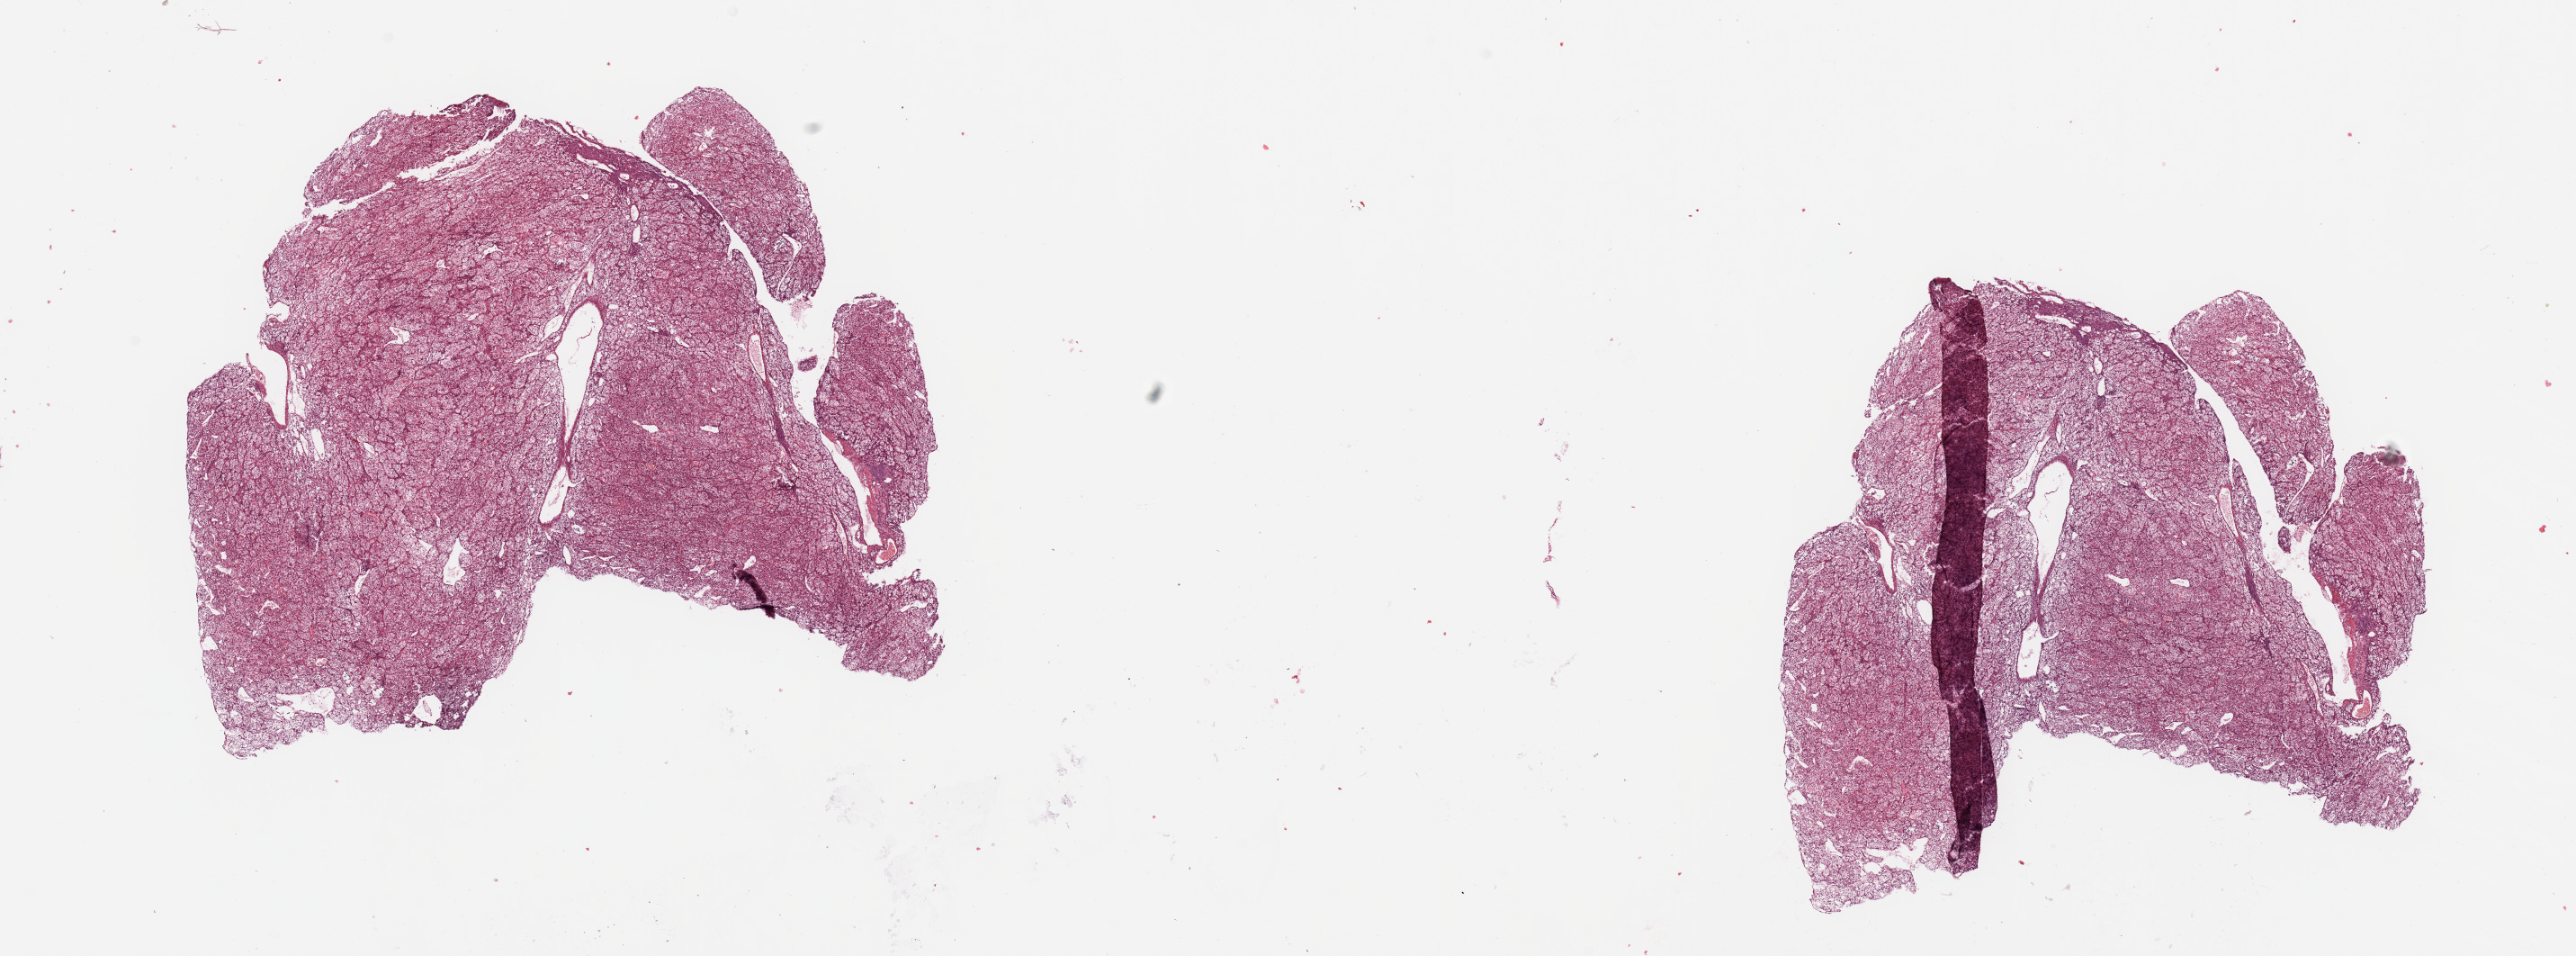
Hematoxylin and eosin (H&E) stained whole-slide image — a low-resolution overview of the entire scanned area, about 22.6 x 8.4 mm (slide scanned at 20x); tumour tissue sample, sampled site: kidney. Patient: female, age 58 years. Histologic grade: G2 (moderately differentiated). Slide review estimates, as recorded: tumour nuclei 95%, necrosis 0%.
AJCC pathologic stage: III. Histologic diagnosis: Renal cell carcinoma, NOS. Primary tumour site (as recorded): middle.